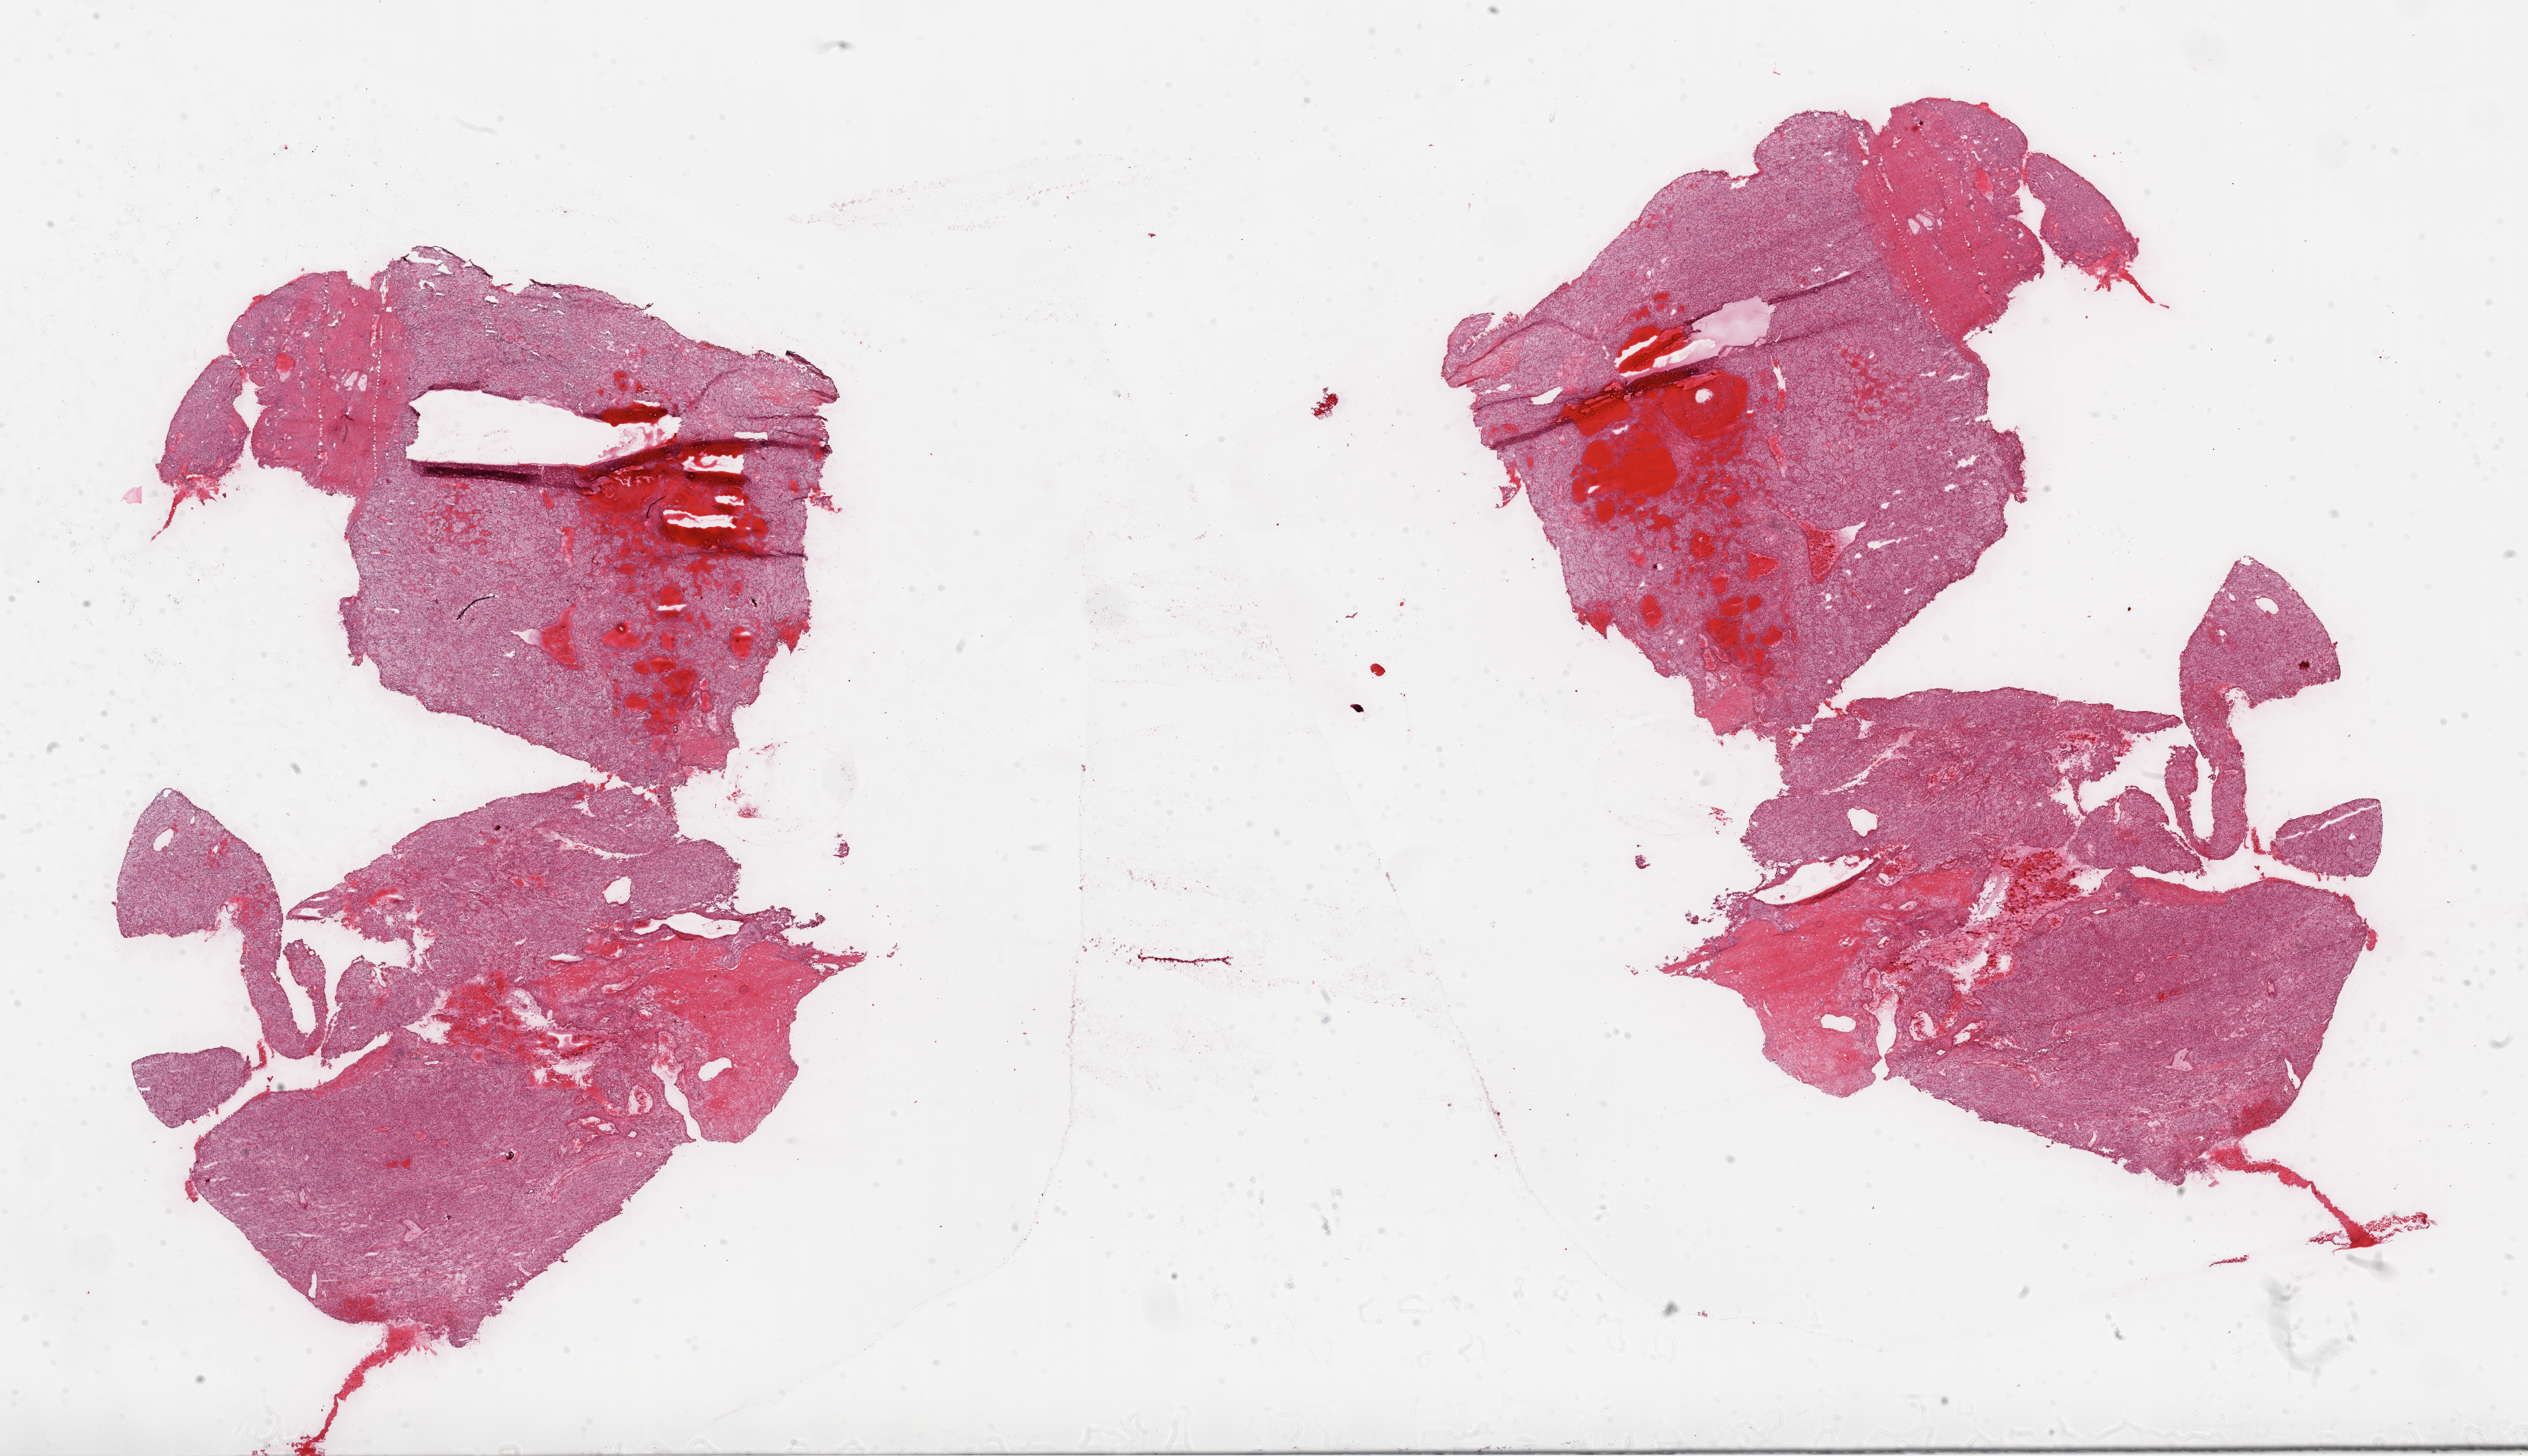
Whole-slide histology image, H&E-stained — low-resolution overview of the scanned area, about 32.1 x 18.5 mm. Frozen section from the top of the tissue portion. Primary tumour sample from the kidney. Male, age 40 years at initial diagnosis. Histologic grade: G3 (poorly differentiated). Slide review estimates, as recorded: tumour cells 80%, tumour nuclei 80%, normal cells 10%, stromal cells 10%, necrosis 0%.
Histologic diagnosis: Clear cell adenocarcinoma, NOS. AJCC pathologic stage: I.